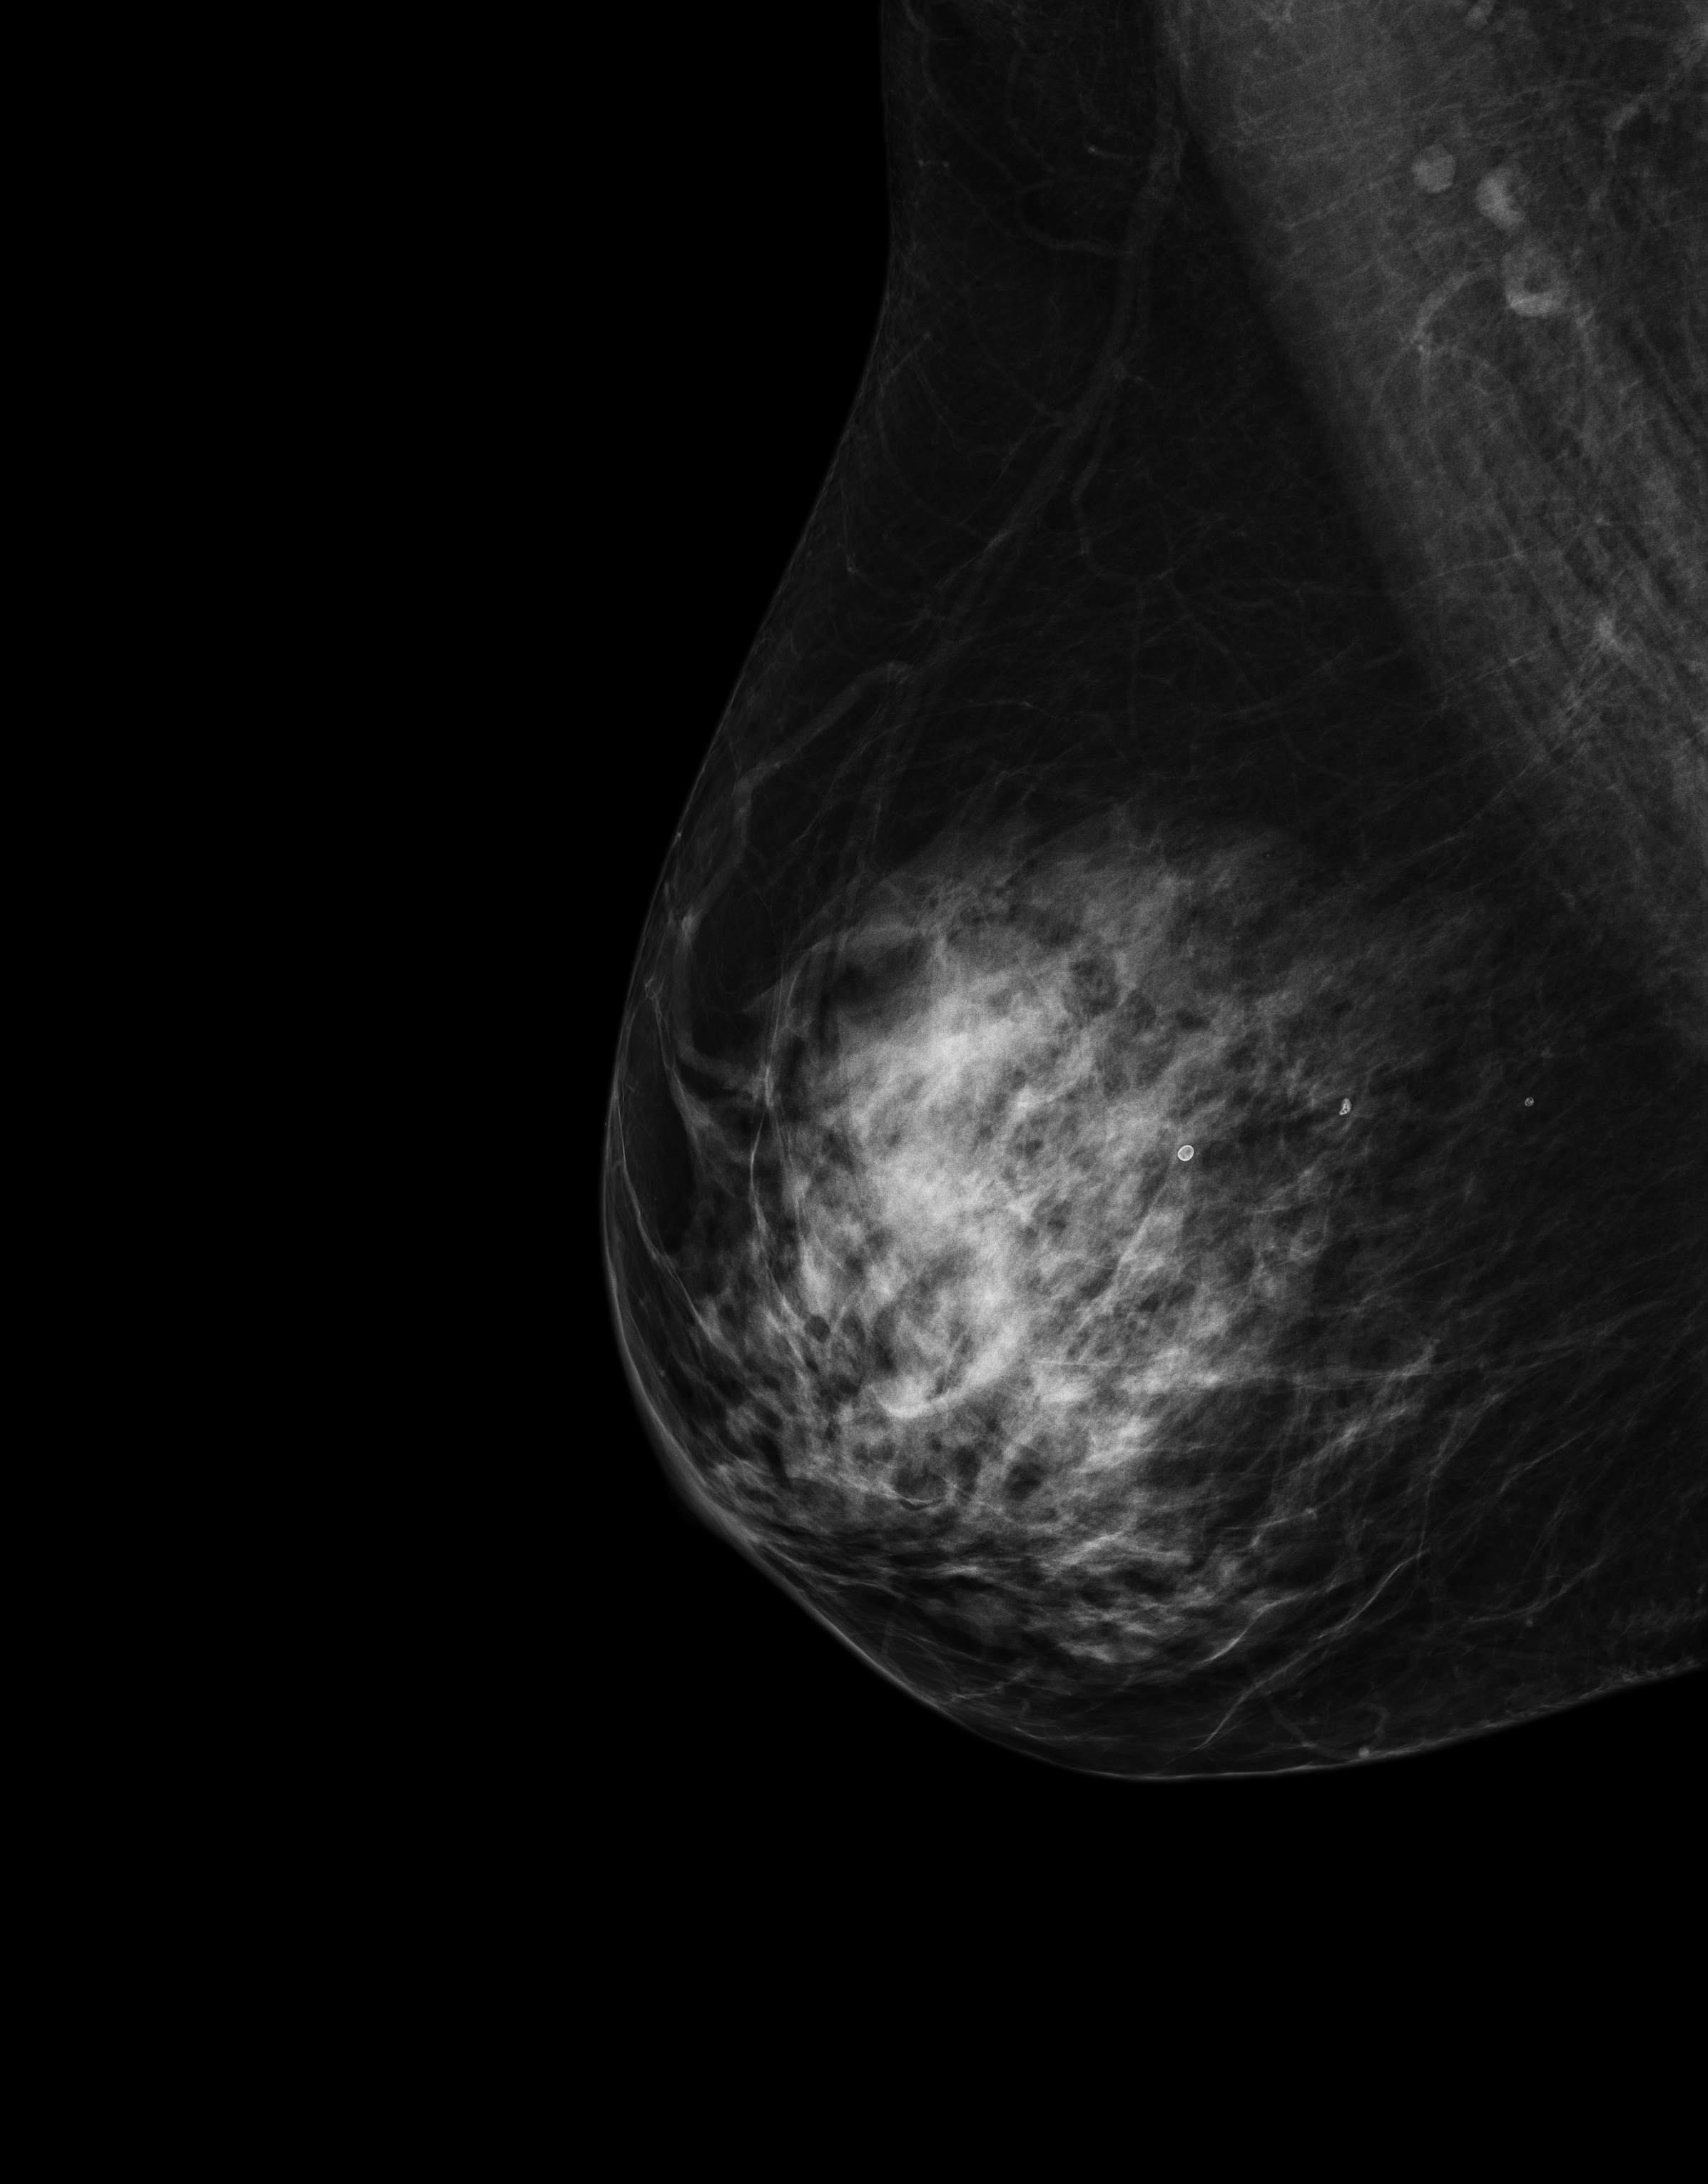
Screening examination. Patient: female, 65 years.
Image type: full-field digital mammogram. Breast: right. Projection: MLO view. Breast density at the screening exam (both breasts): heterogeneously dense (BI-RADS density category c). Final BI-RADS category for the screening round (tomosynthesis exam, both breasts): category 1. Recall: no recall after this screen.